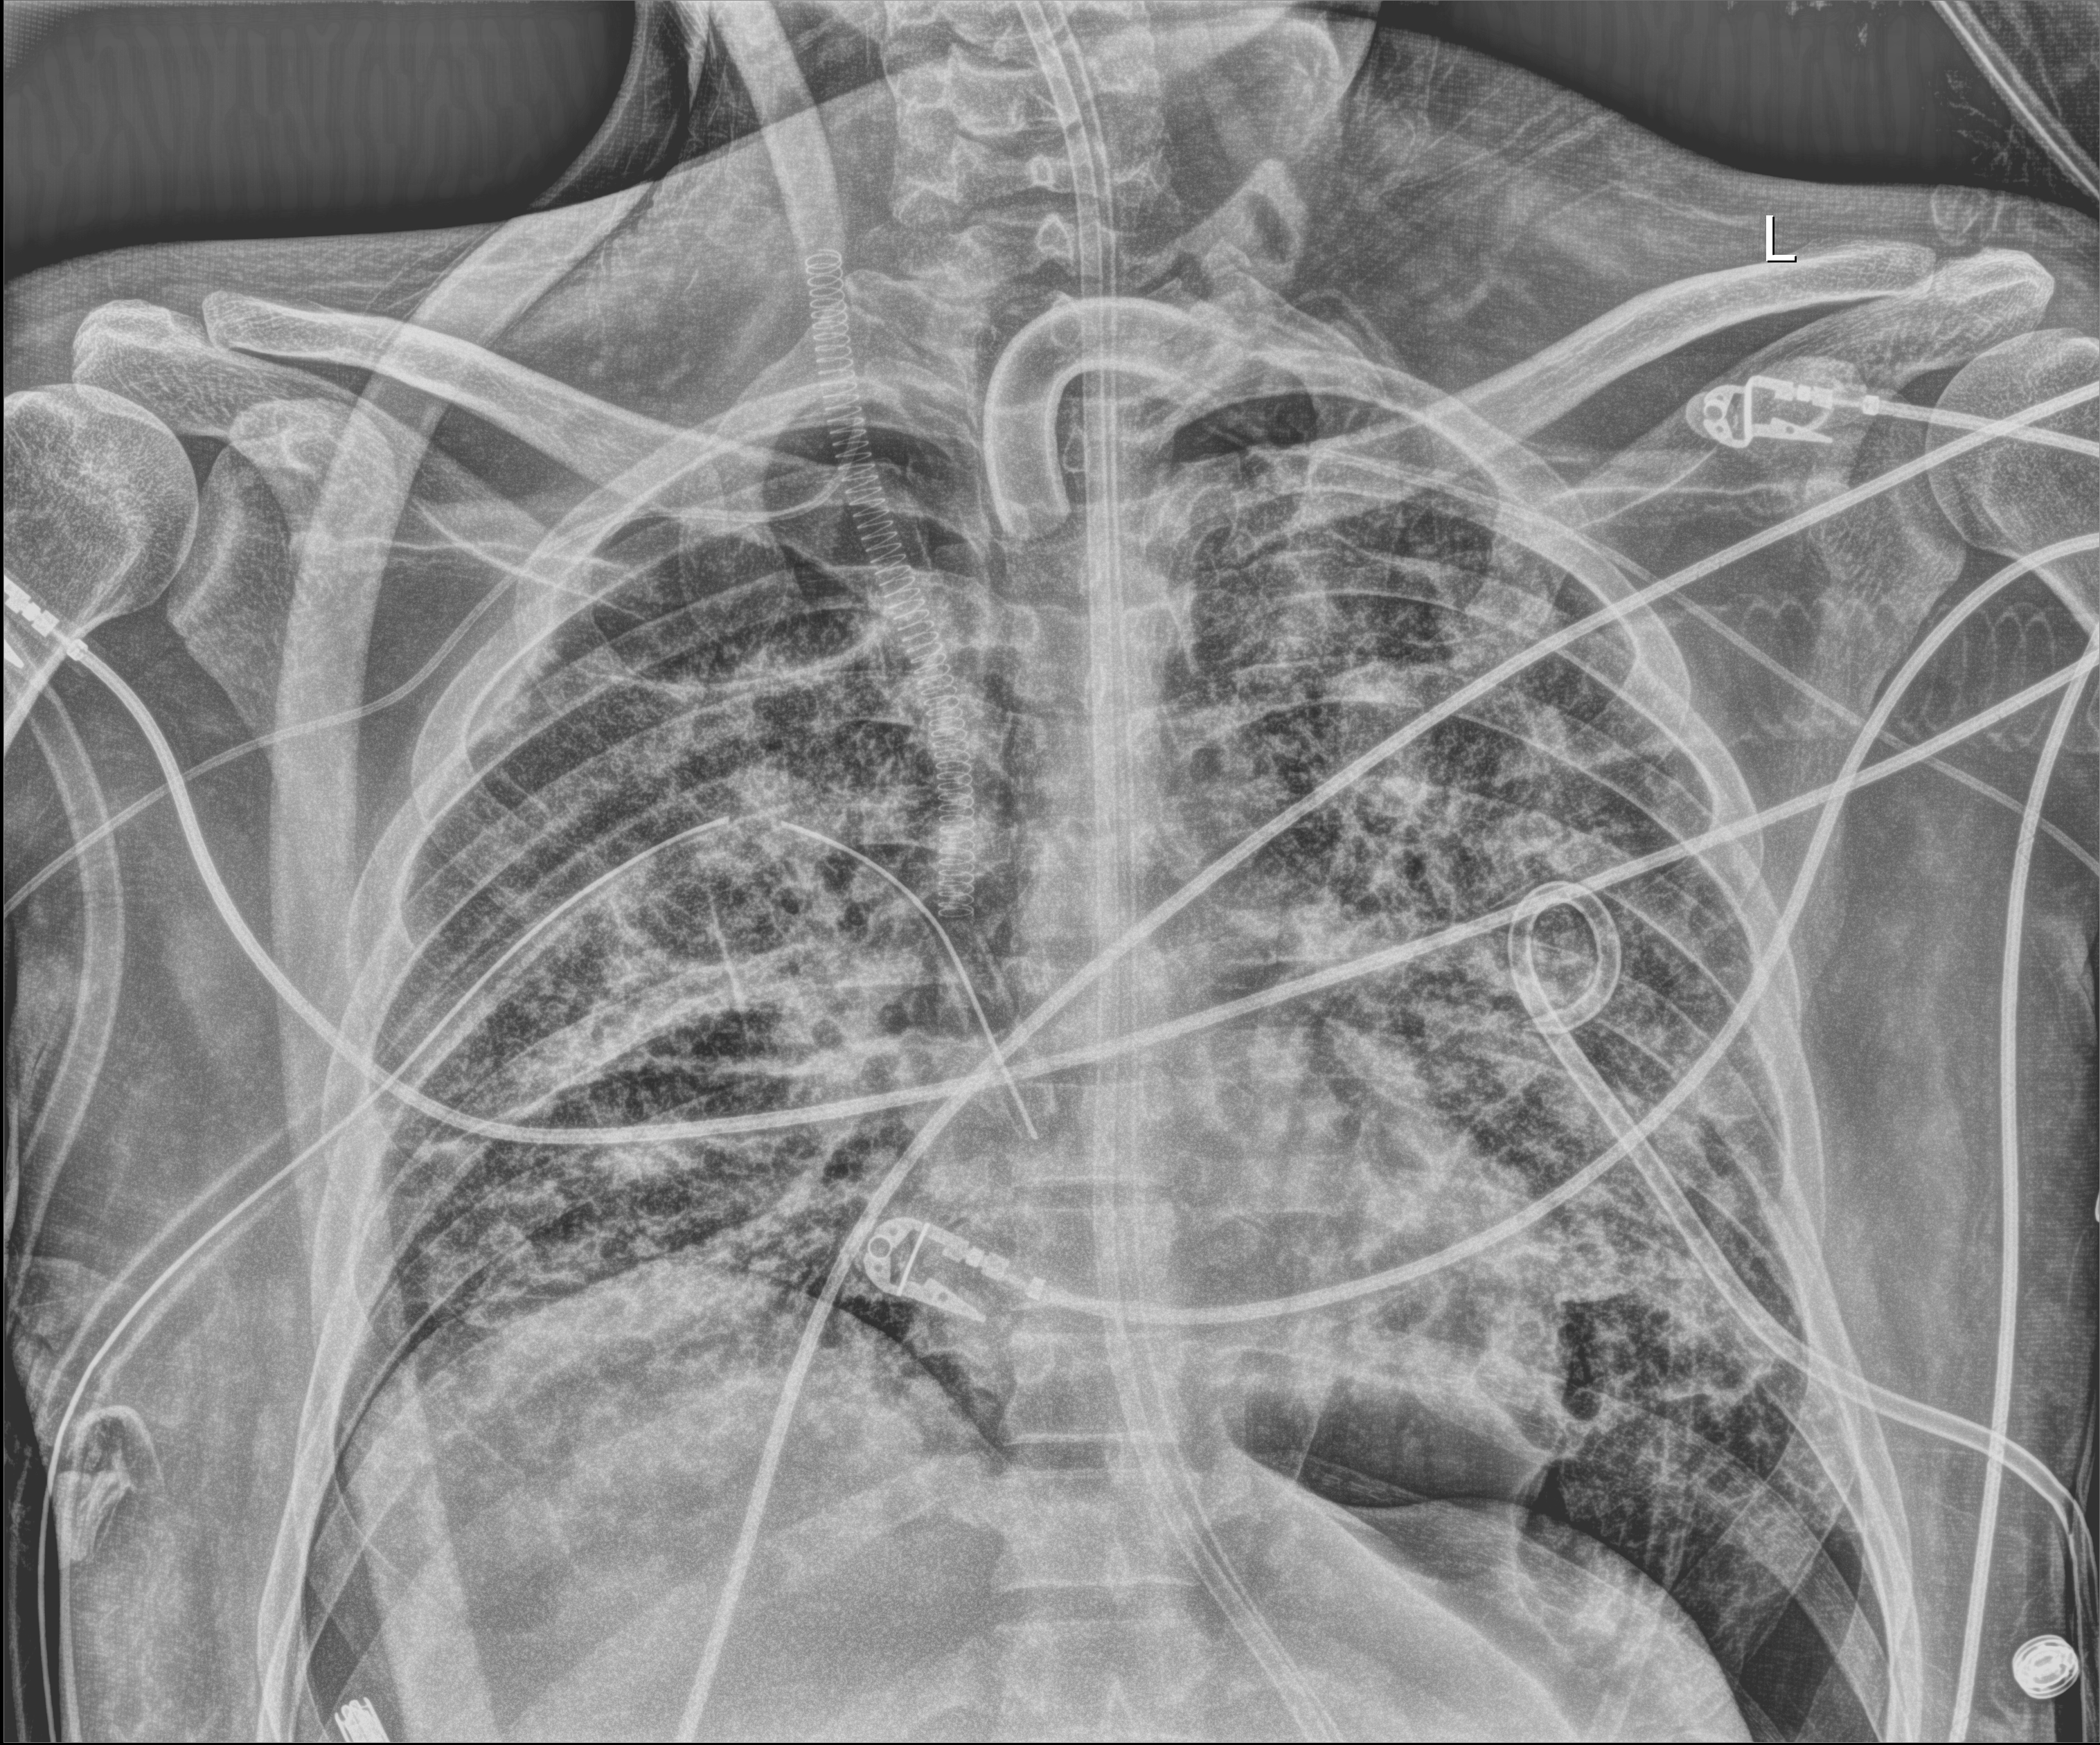
Chest radiograph (digital radiography), anteroposterior (AP) projection. Adult patient hospitalised with COVID-19, age 18–59 years.
Hospital-stay facts (about this admission, not read from this image; timing relative to this image not recorded): hypertension (admission record): no.